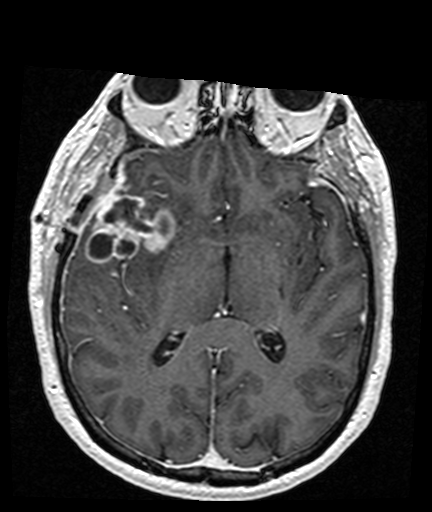
Brain MRI from a brain-tumour surgery series, one axial slice. Position 86 of 176 along the scan axis. T1-weighted post-contrast. 432 × 512 image matrix, field of view 194 × 230 mm. From the clinical record (not read from this slice): histopathology: Glioblastoma; WHO grade: 4; IDH mutation: no.
Outlined on this slice (expert manual segmentation):
- tumour: bounding box [x1, y1, x2, y2] px = [85, 185, 175, 264]